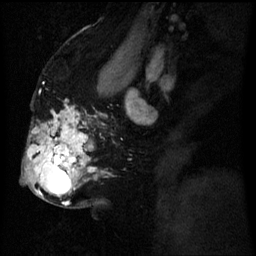
Breast MRI (dynamic contrast-enhanced), one sagittal slice. Position 35 of 60 along the scan axis. Dynamic contrast-enhanced series, image 2 of 3 at this slice position (ordered by acquisition). 1.5 T. TE 4.2 ms, TR 8 ms. 2.5 mm slice thickness. 256 × 256 image matrix, field of view 200 × 200 mm. Female patient, age 50 years.
Structures marked on this image (semi-automatically segmented with operator editing):
- analysis volume of interest (the breast-tissue region the enhancement analysis was run in; not a lesion): bounding box [x1, y1, x2, y2] px = [25, 112, 92, 203]
- tumour enhancement mask (voxels above the 70 % enhancement threshold inside the analysis volume of interest): [31, 120, 92, 203]